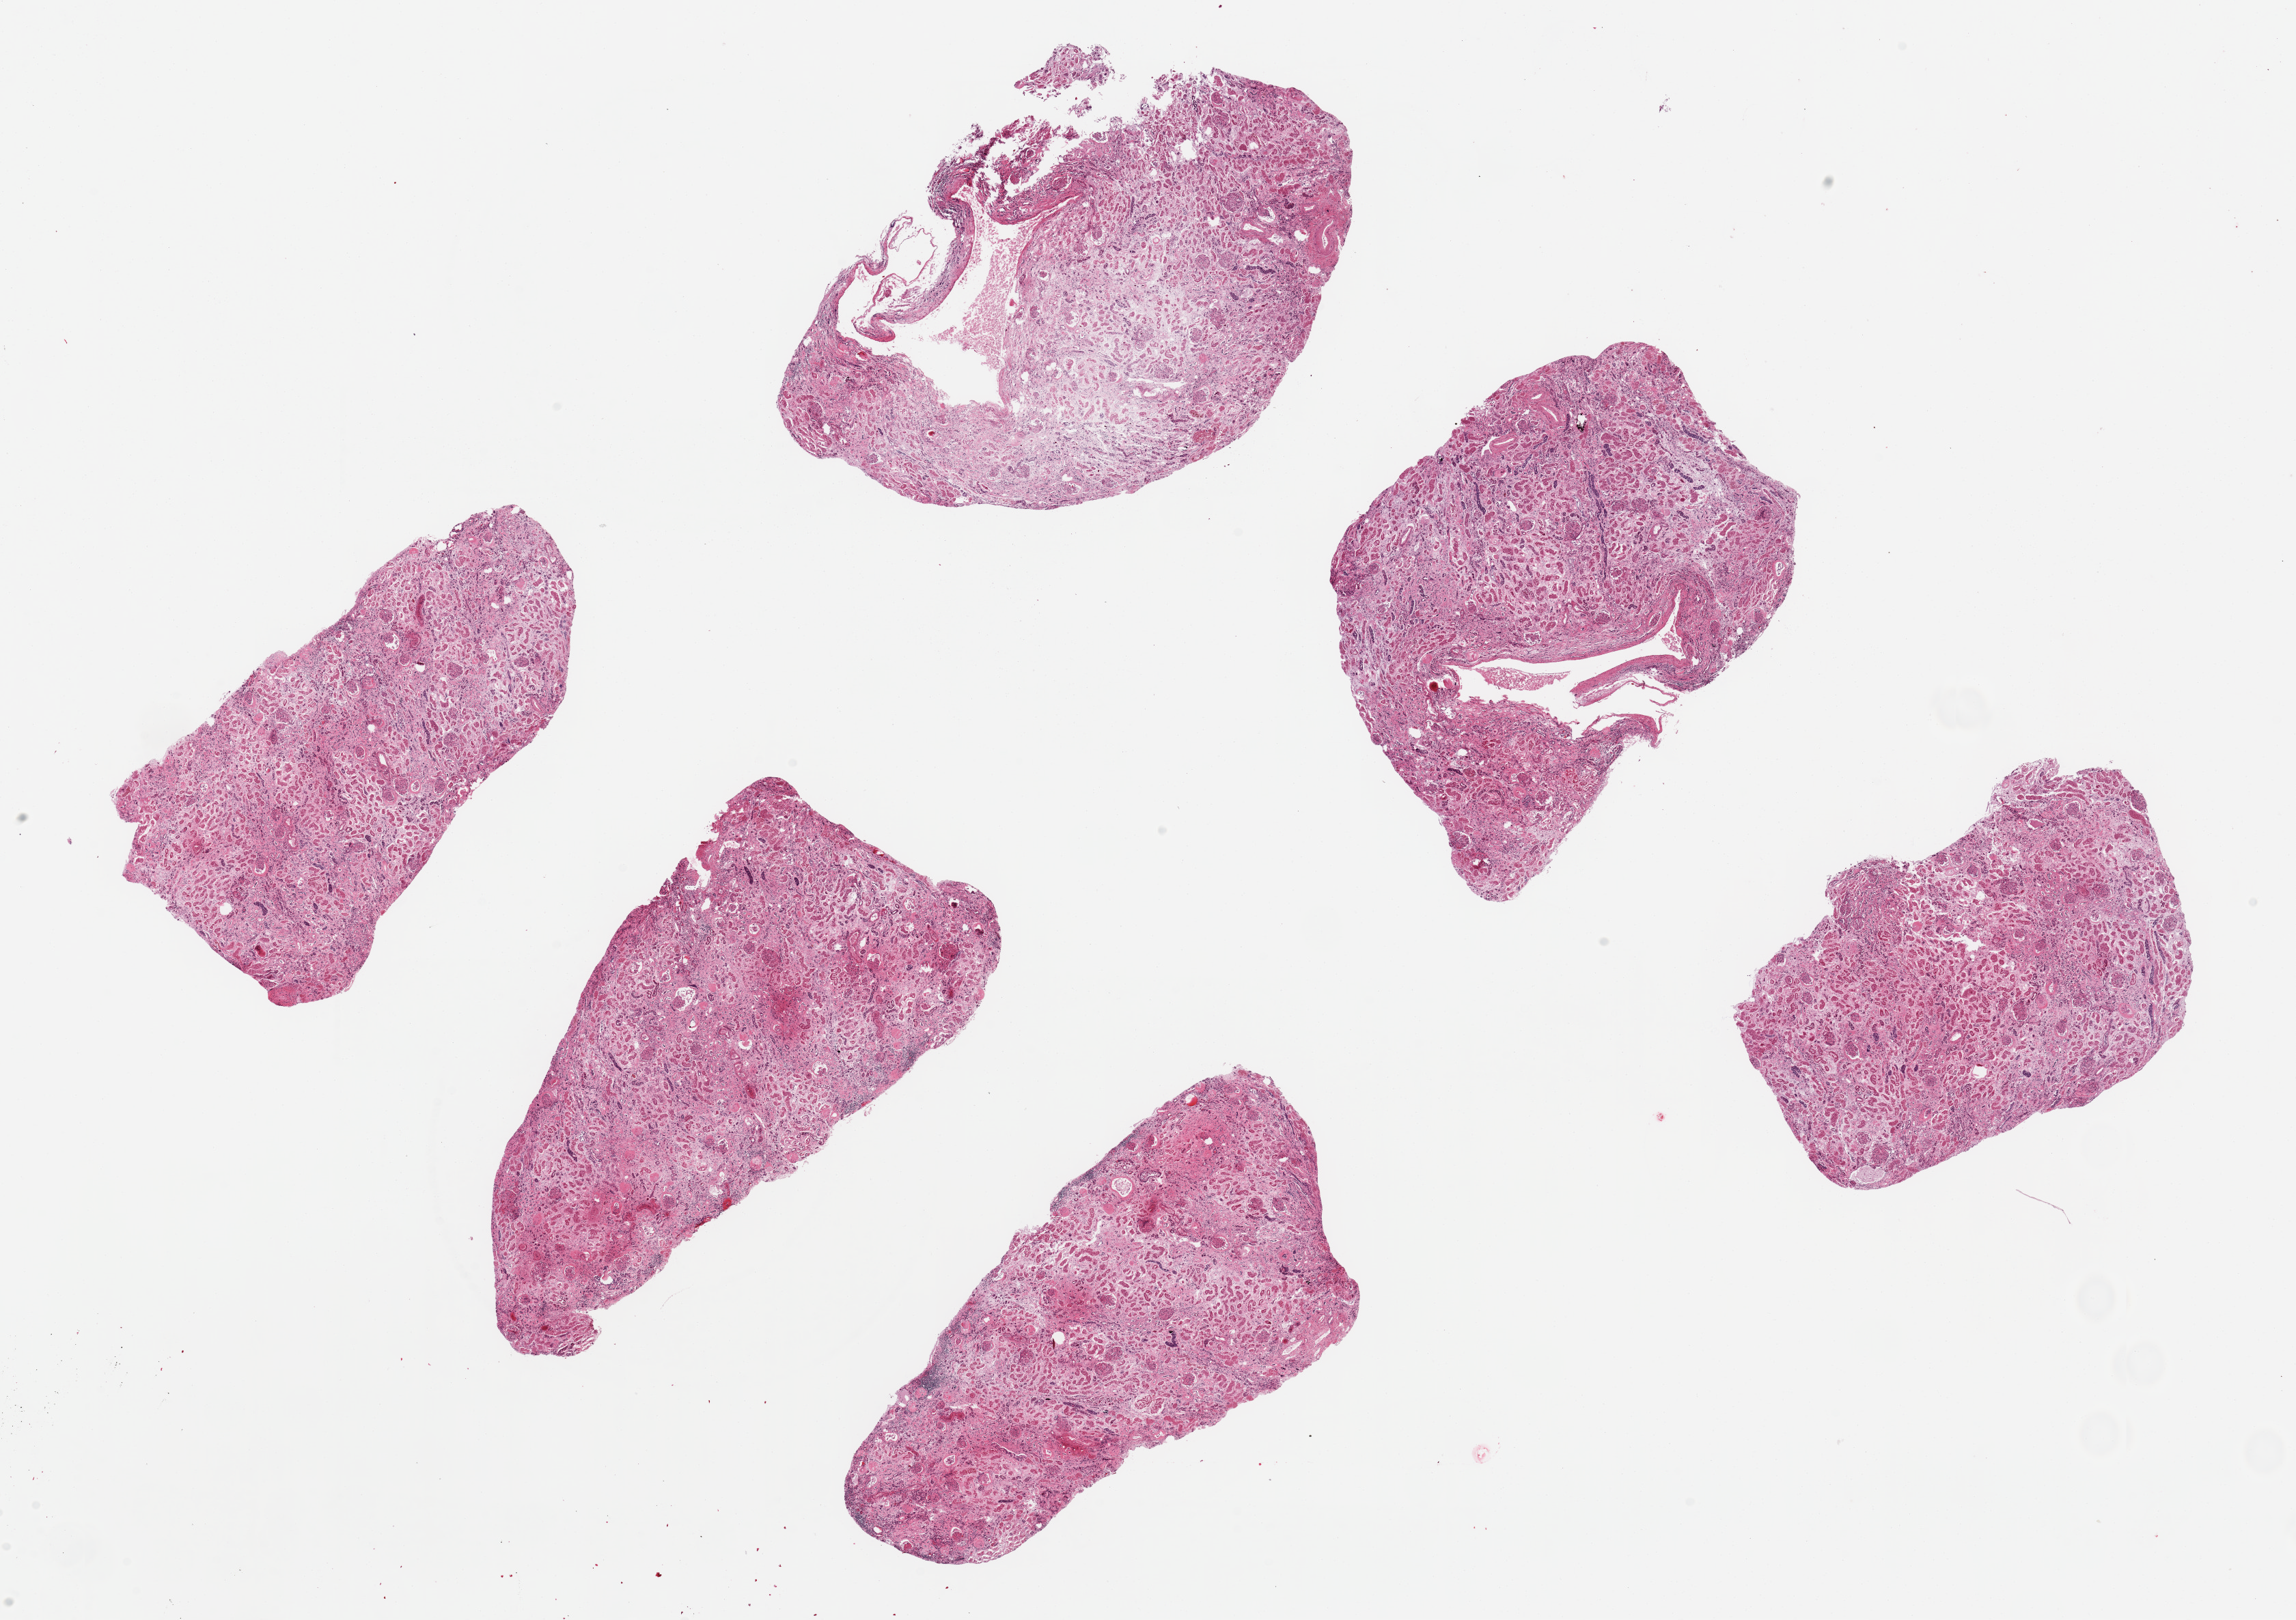
Digitized hematoxylin and eosin (H&E)-stained section, whole scanned area (about 26.6 x 18.8 mm, acquisition: 20x scan) shown as a low-resolution overview. PAXgene-fixed paraffin-embedded (PFPE) section. Target tissue: renal cortex. Donor tissue sample. Donor: male.
Reviewer comment on this tissue sample: 6 ~ 6.5x3mm pieces. Marked tubular and moderate-marked glomerular autolysis, / ? infarction in one aliquot.